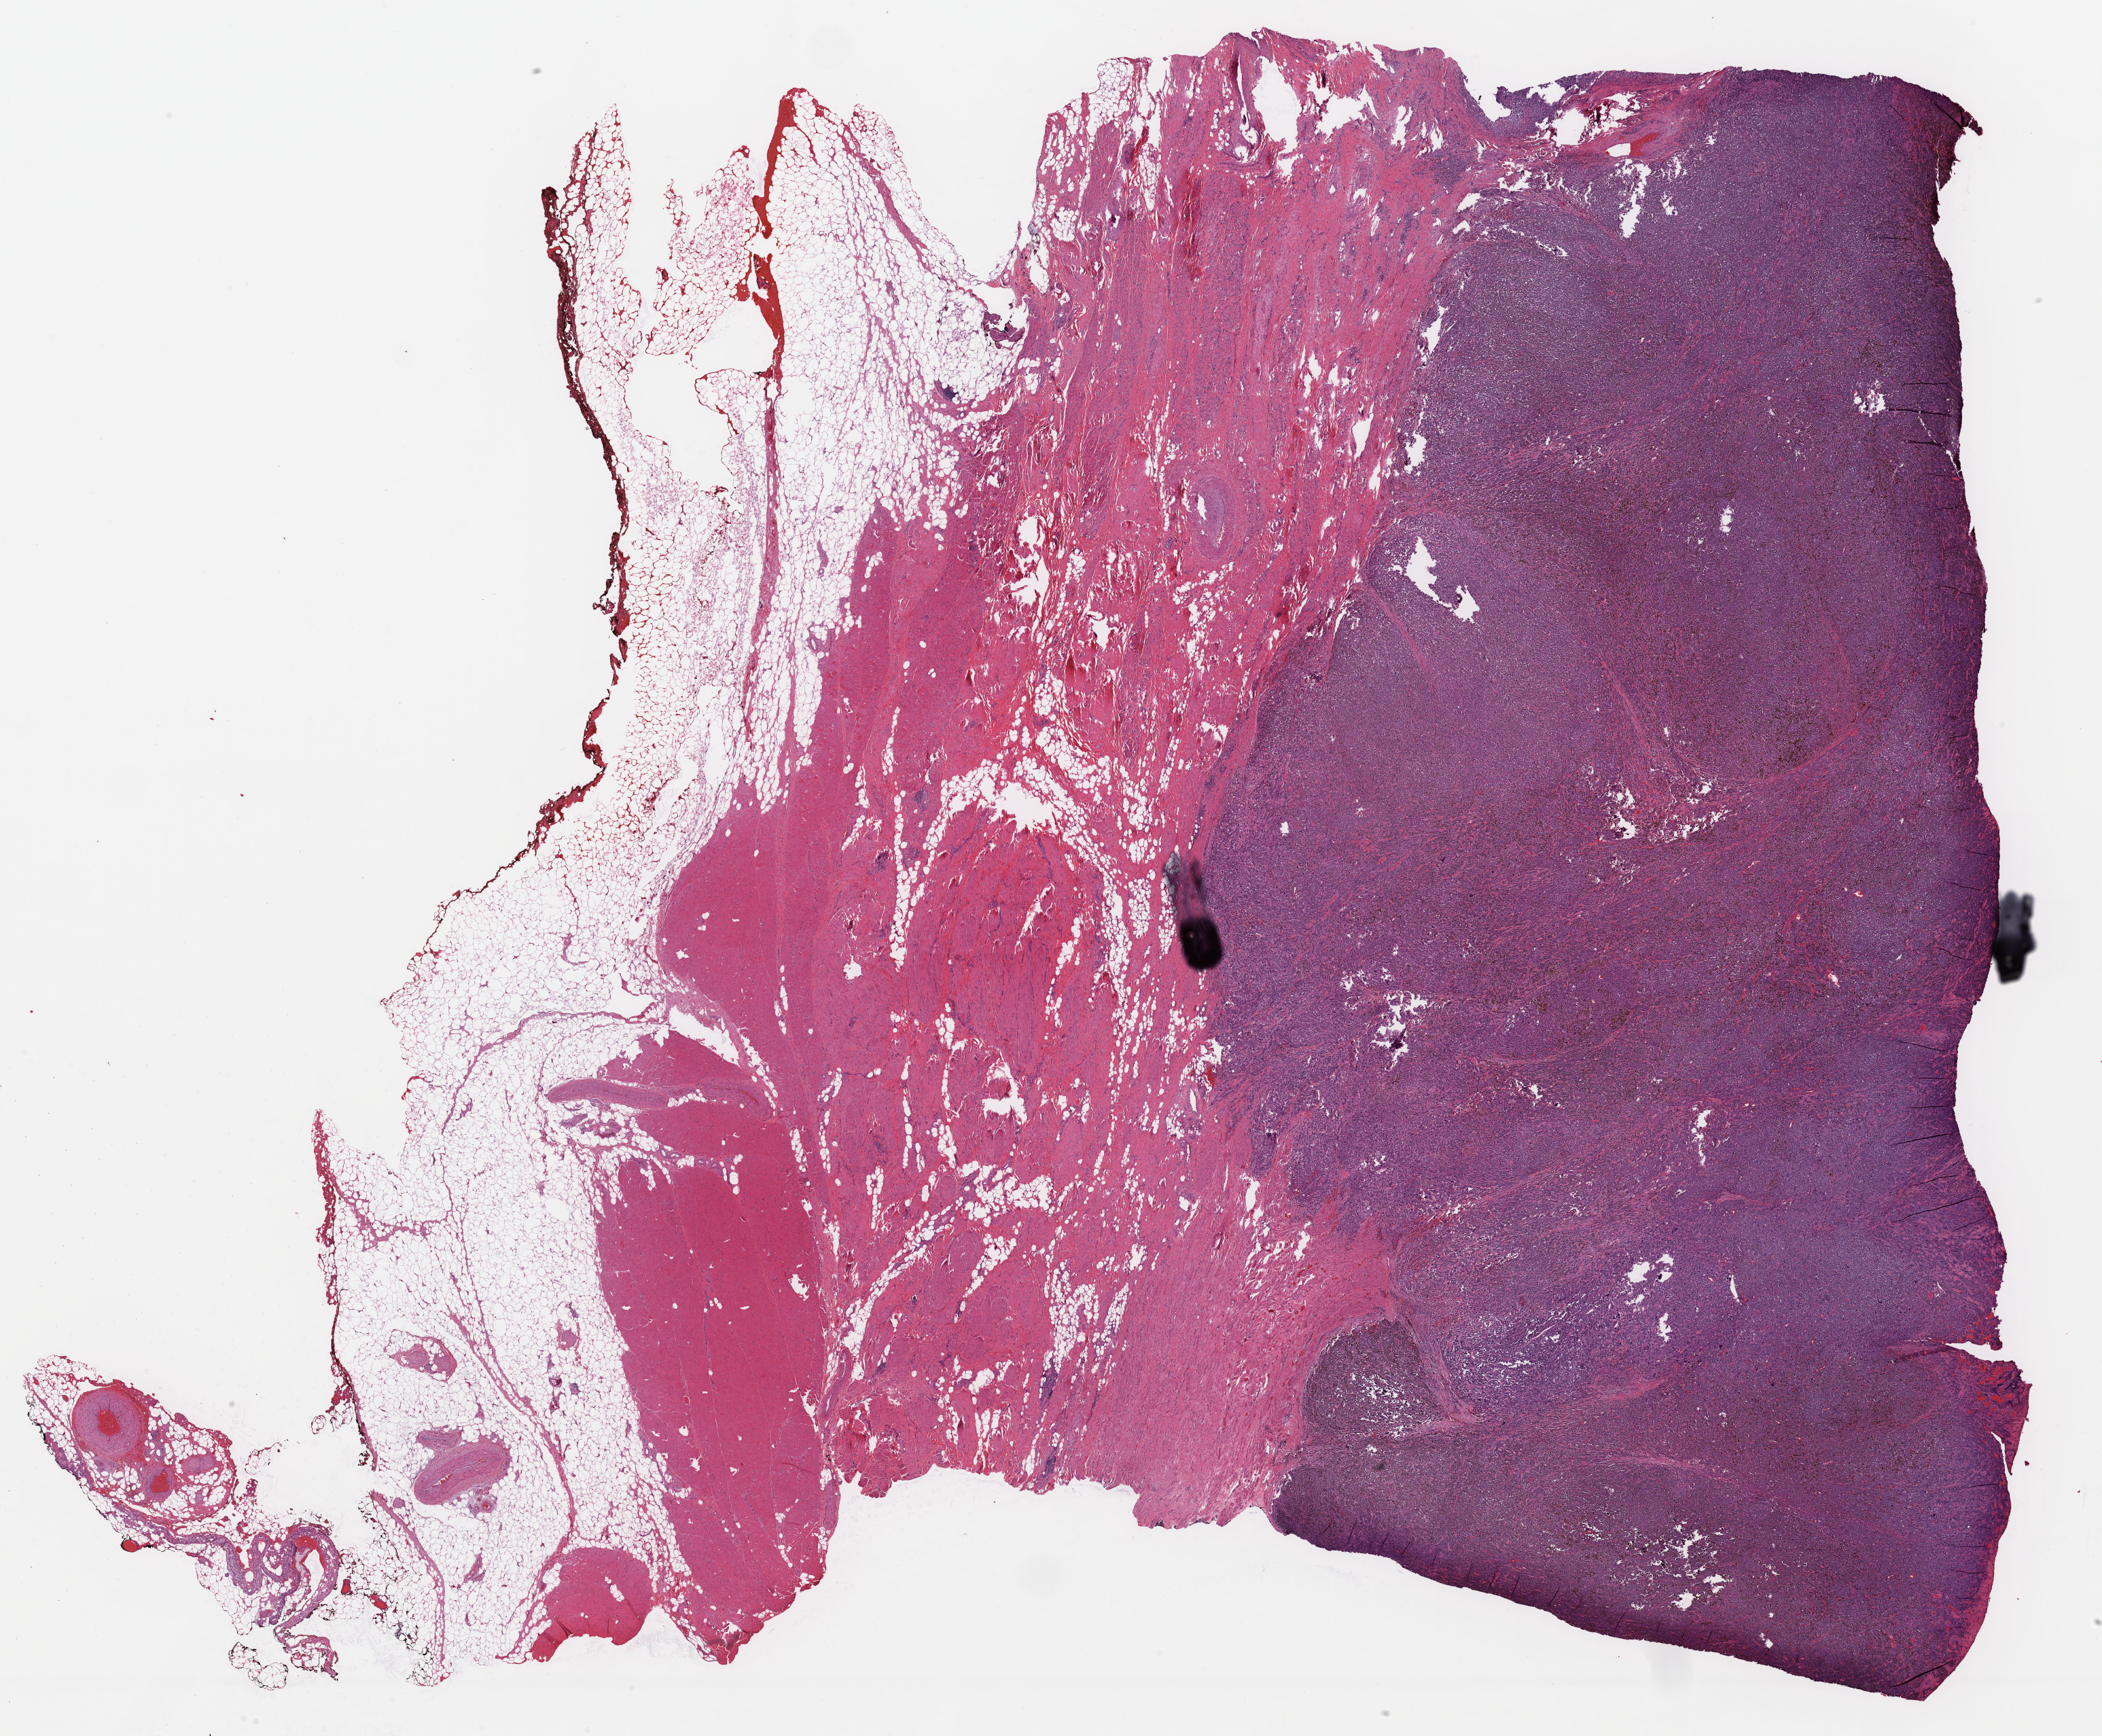
Digitized H&E-stained tissue section (whole slide) — a low-resolution overview of the entire scanned area, about 24.4 x 20.2 mm (acquisition: 40x scan). Formalin-fixed paraffin-embedded (FFPE) diagnostic section. Skin, primary tumour sample. Male, age 57 years at initial diagnosis.
Pathologic diagnosis: Malignant melanoma, NOS.